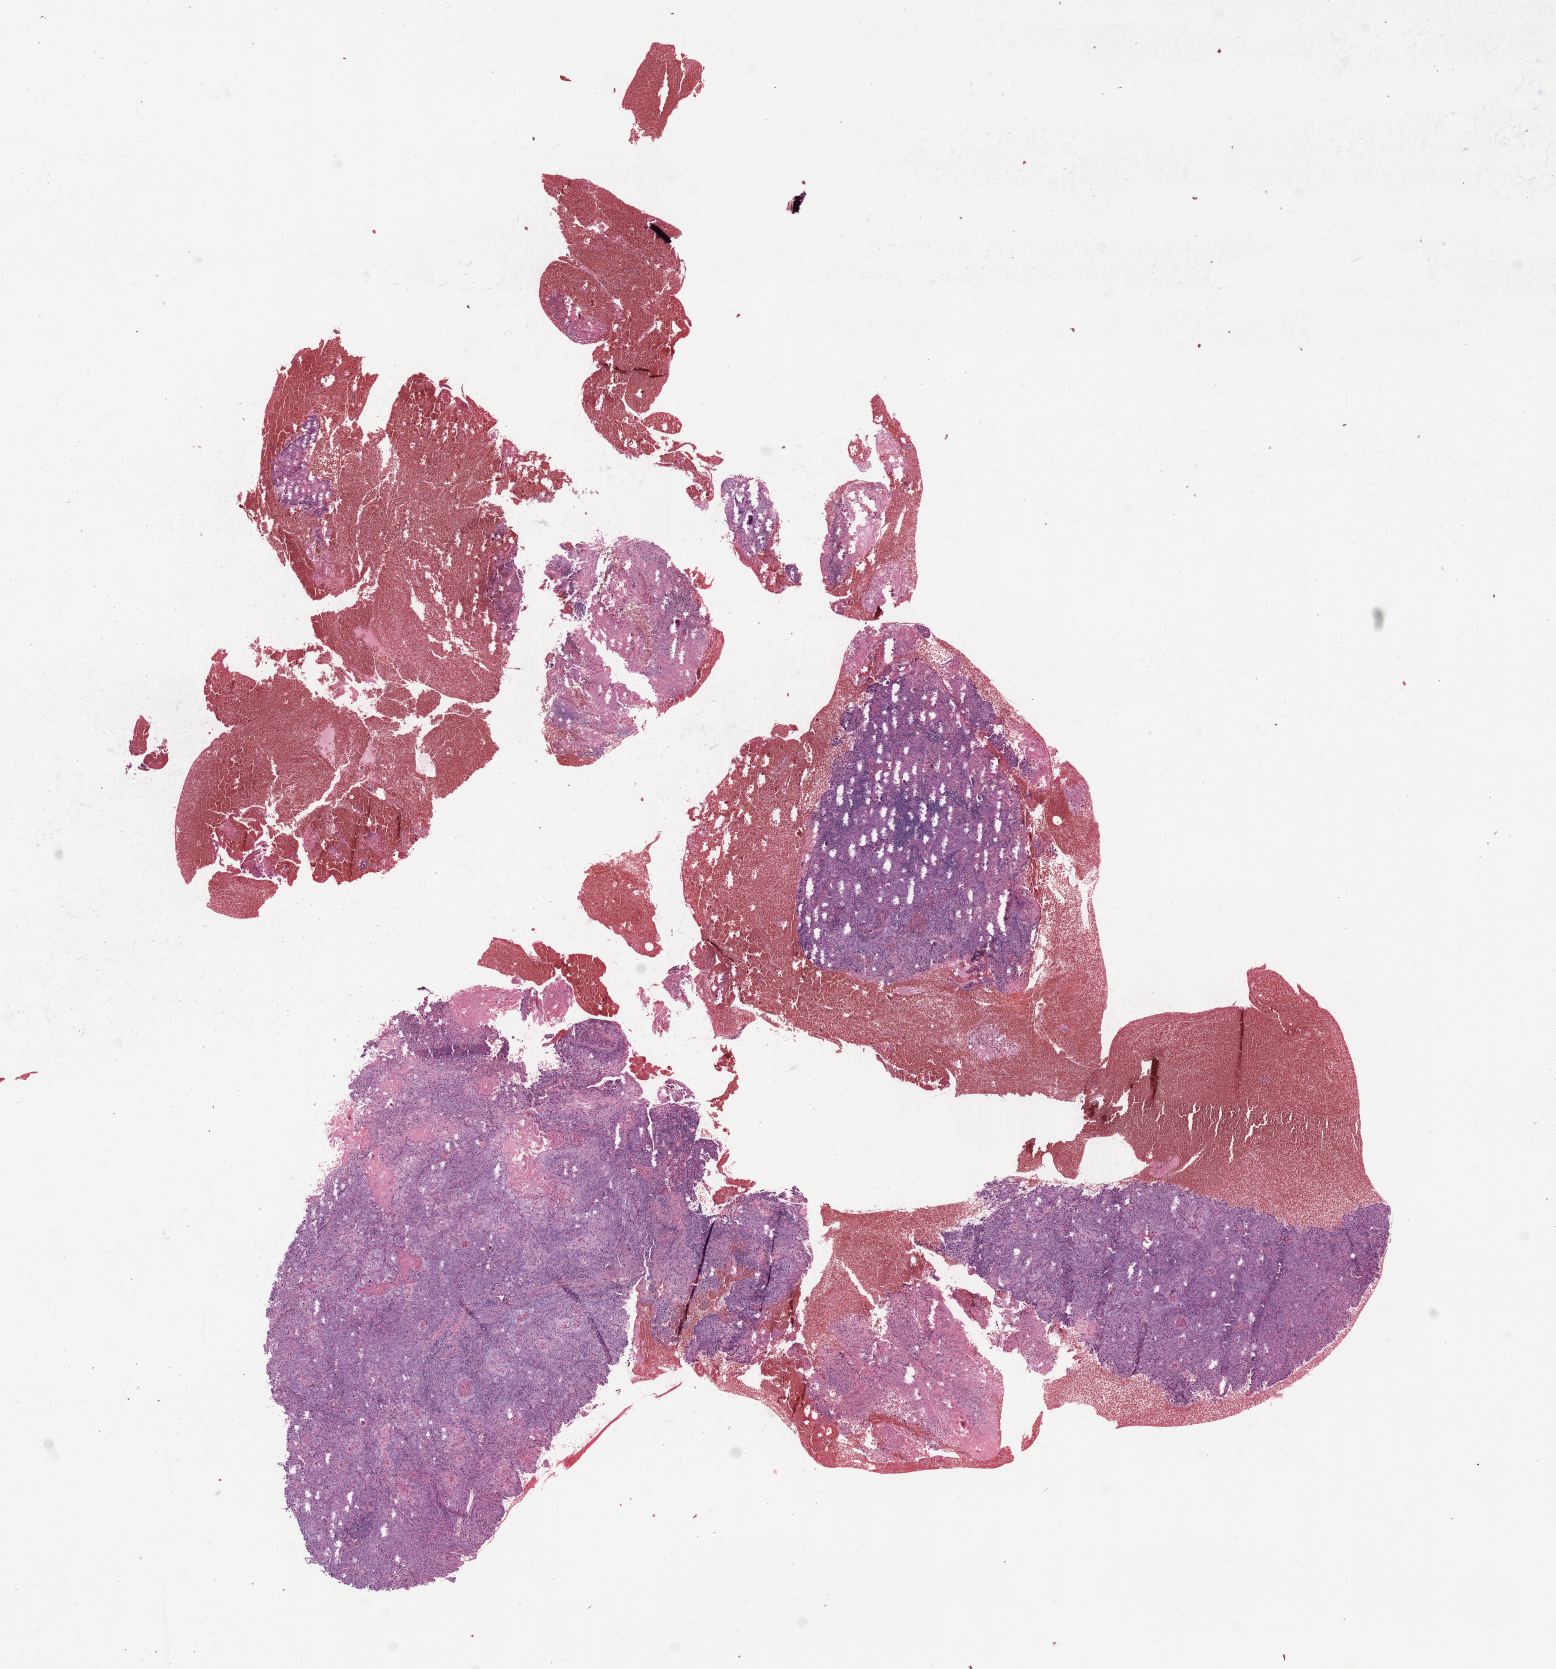
Whole-slide histology image, H&E-stained — shown as a low-resolution overview of the whole scanned area (about 12.6 x 13.5 mm, acquisition: 40x scan); FFPE section; primary tumour sample from the cervix. Patient: female, age at initial diagnosis 53 years.
Histologic diagnosis: Squamous cell carcinoma, NOS (cervix uteri).